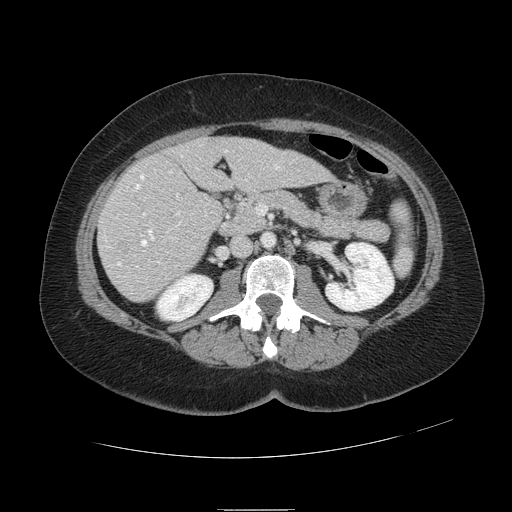
Contrast-enhanced abdominal CT, one axial slice; position 40 of 121 along the scan axis; soft-tissue window (W 400 / L 40 HU); 2.5 mm slice thickness; 512 × 512 image matrix, field of view 400 × 400 mm. Female patient, age 52 years. From the clinical record (not read from this slice): diagnosis: colorectal cancer liver metastases, imaged before liver resection; multiple liver metastases: yes; largest metastasis: 6.3 cm.
Annotated regions visible in this slice (expert manual segmentation):
- hepatic veins: bounding box <117,150,279,266> (left, top, right, bottom; pixels)
- liver: <100,137,331,302>
- planned liver remnant (the part of the liver to remain after resection): <178,136,331,193>
- portal vein (with intrahepatic branches): <143,196,180,216>